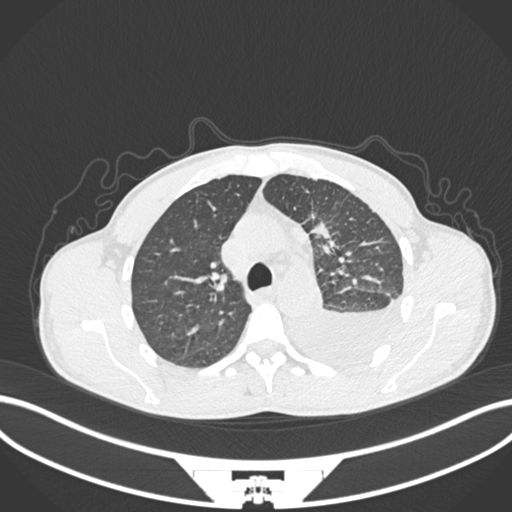
Chest CT, one axial slice; slice 151 of 244 in the series (ordered by position); reconstruction kernel B30f; lung window (W 1500 / L -600 HU); 1 mm slice thickness; 512 × 512 image matrix, field of view 400 × 400 mm. Patient: male, 49 years. From the clinical record (not read from this slice): clinical TNM (as recorded): T1c N1 M1.
Structures marked on this image (rectangle marked by the reading radiologist):
- lung tumour (recorded histology: adenocarcinoma): box from (x=303, y=208) to (x=336, y=250) px